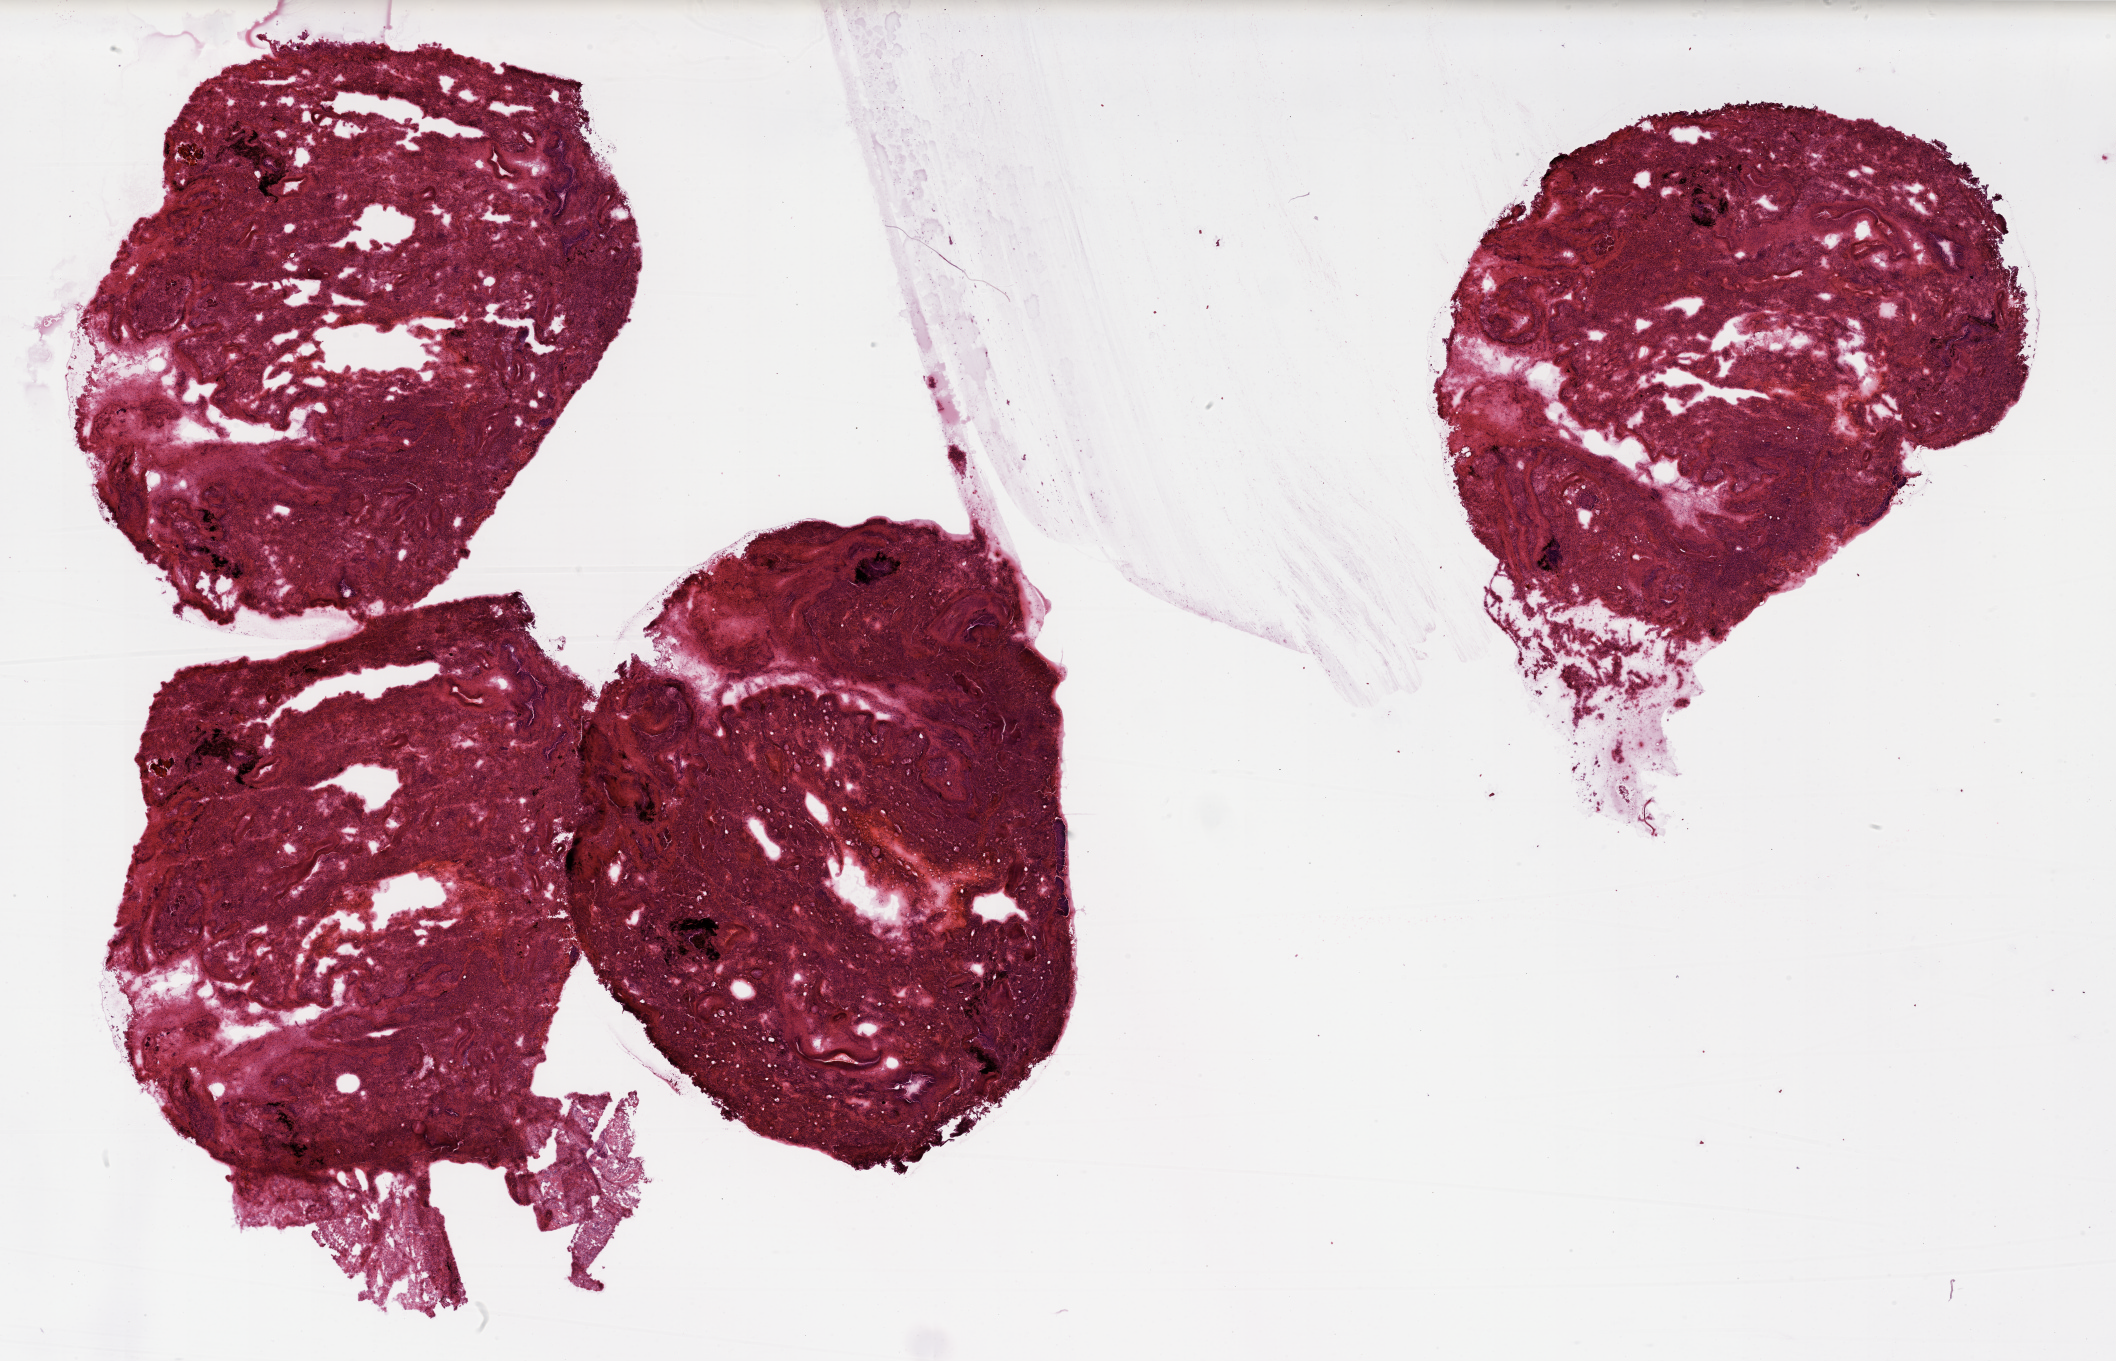
H&E whole-slide image, shown as a low-resolution overview of the whole scanned area (about 33.5 x 21.5 mm, acquisition: 20x scan), lung, normal (non-tumour) tissue. Patient: male, age 65 years.
This section: normal (non-tumour) tissue from the same patient. Patient diagnosis (cohort enrolment): squamous cell carcinoma (lung).